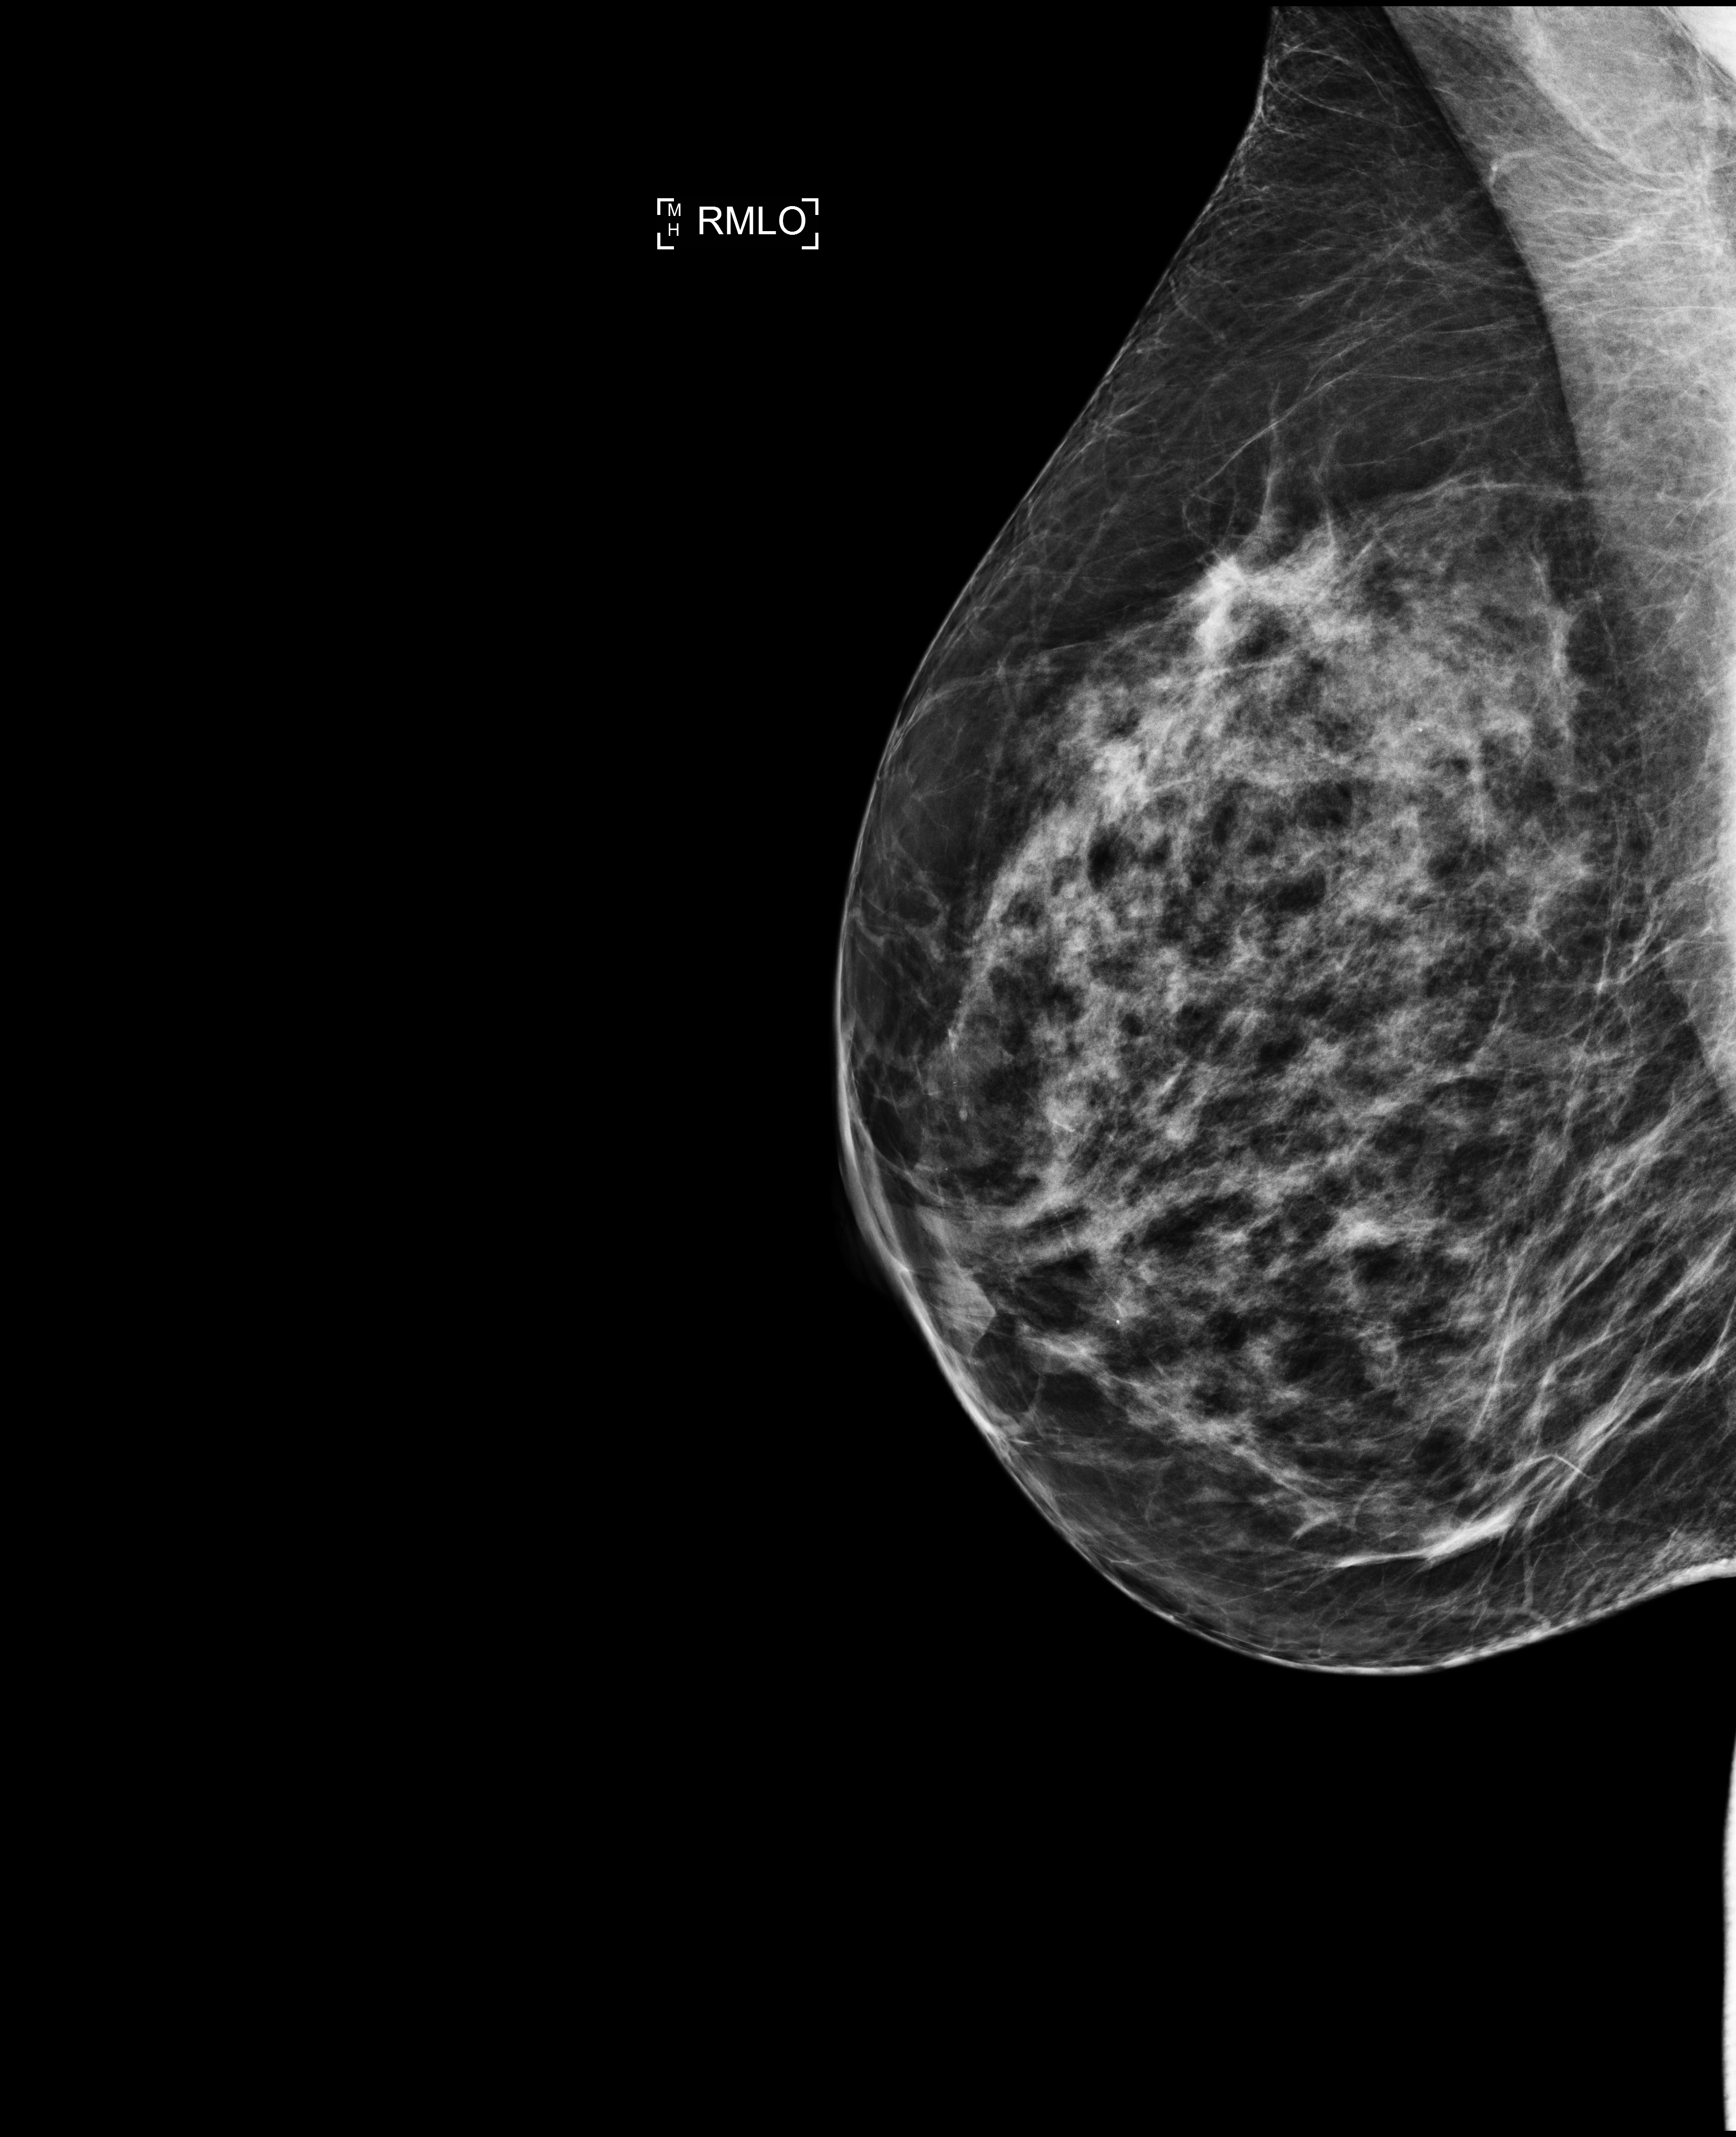
Annual screening mammography examination. Female patient, age 48 years.
Image type: full-field digital mammogram. Breast: right. Projection: mediolateral oblique (MLO) view.